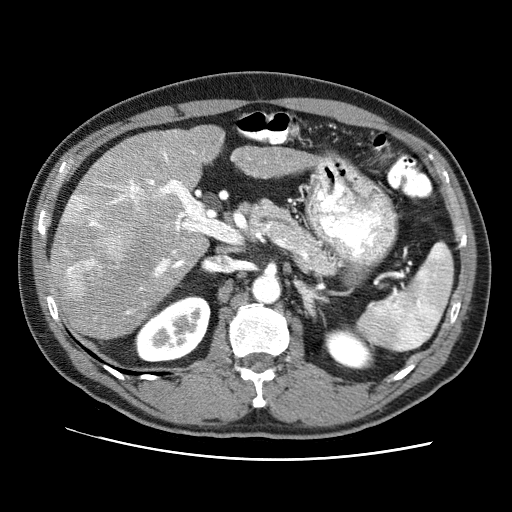
Contrast-enhanced abdominal CT (liver protocol), one axial slice. Slice 43 of 71 in the series (ordered by position). Reconstruction kernel STANDARD. Soft-tissue window (W 400 / L 40 HU). 2.5 mm slice thickness. 512 × 512 image matrix, field of view 360 × 360 mm. From the clinical record (not read from this slice): diagnosis: hepatocellular carcinoma (patient treated with transarterial chemoembolisation; whether this scan precedes or follows treatment is not stated here); TNM stage (as recorded): Stage-II; Child-Pugh class: A; tumour differentiation: well differentiated; tumour size: 4.6 cm.
Structures marked on this image (semi-automatic segmentation, software-assisted and operator-edited):
- liver parenchyma outside the tumour (the mass and vessels are separate outlines, so this box may not span the whole liver): bounding box (x1, y1, x2, y2) in pixels: (50, 124, 318, 340)
- mass: (60, 194, 133, 300)
- liver vessels: (89, 151, 198, 314)